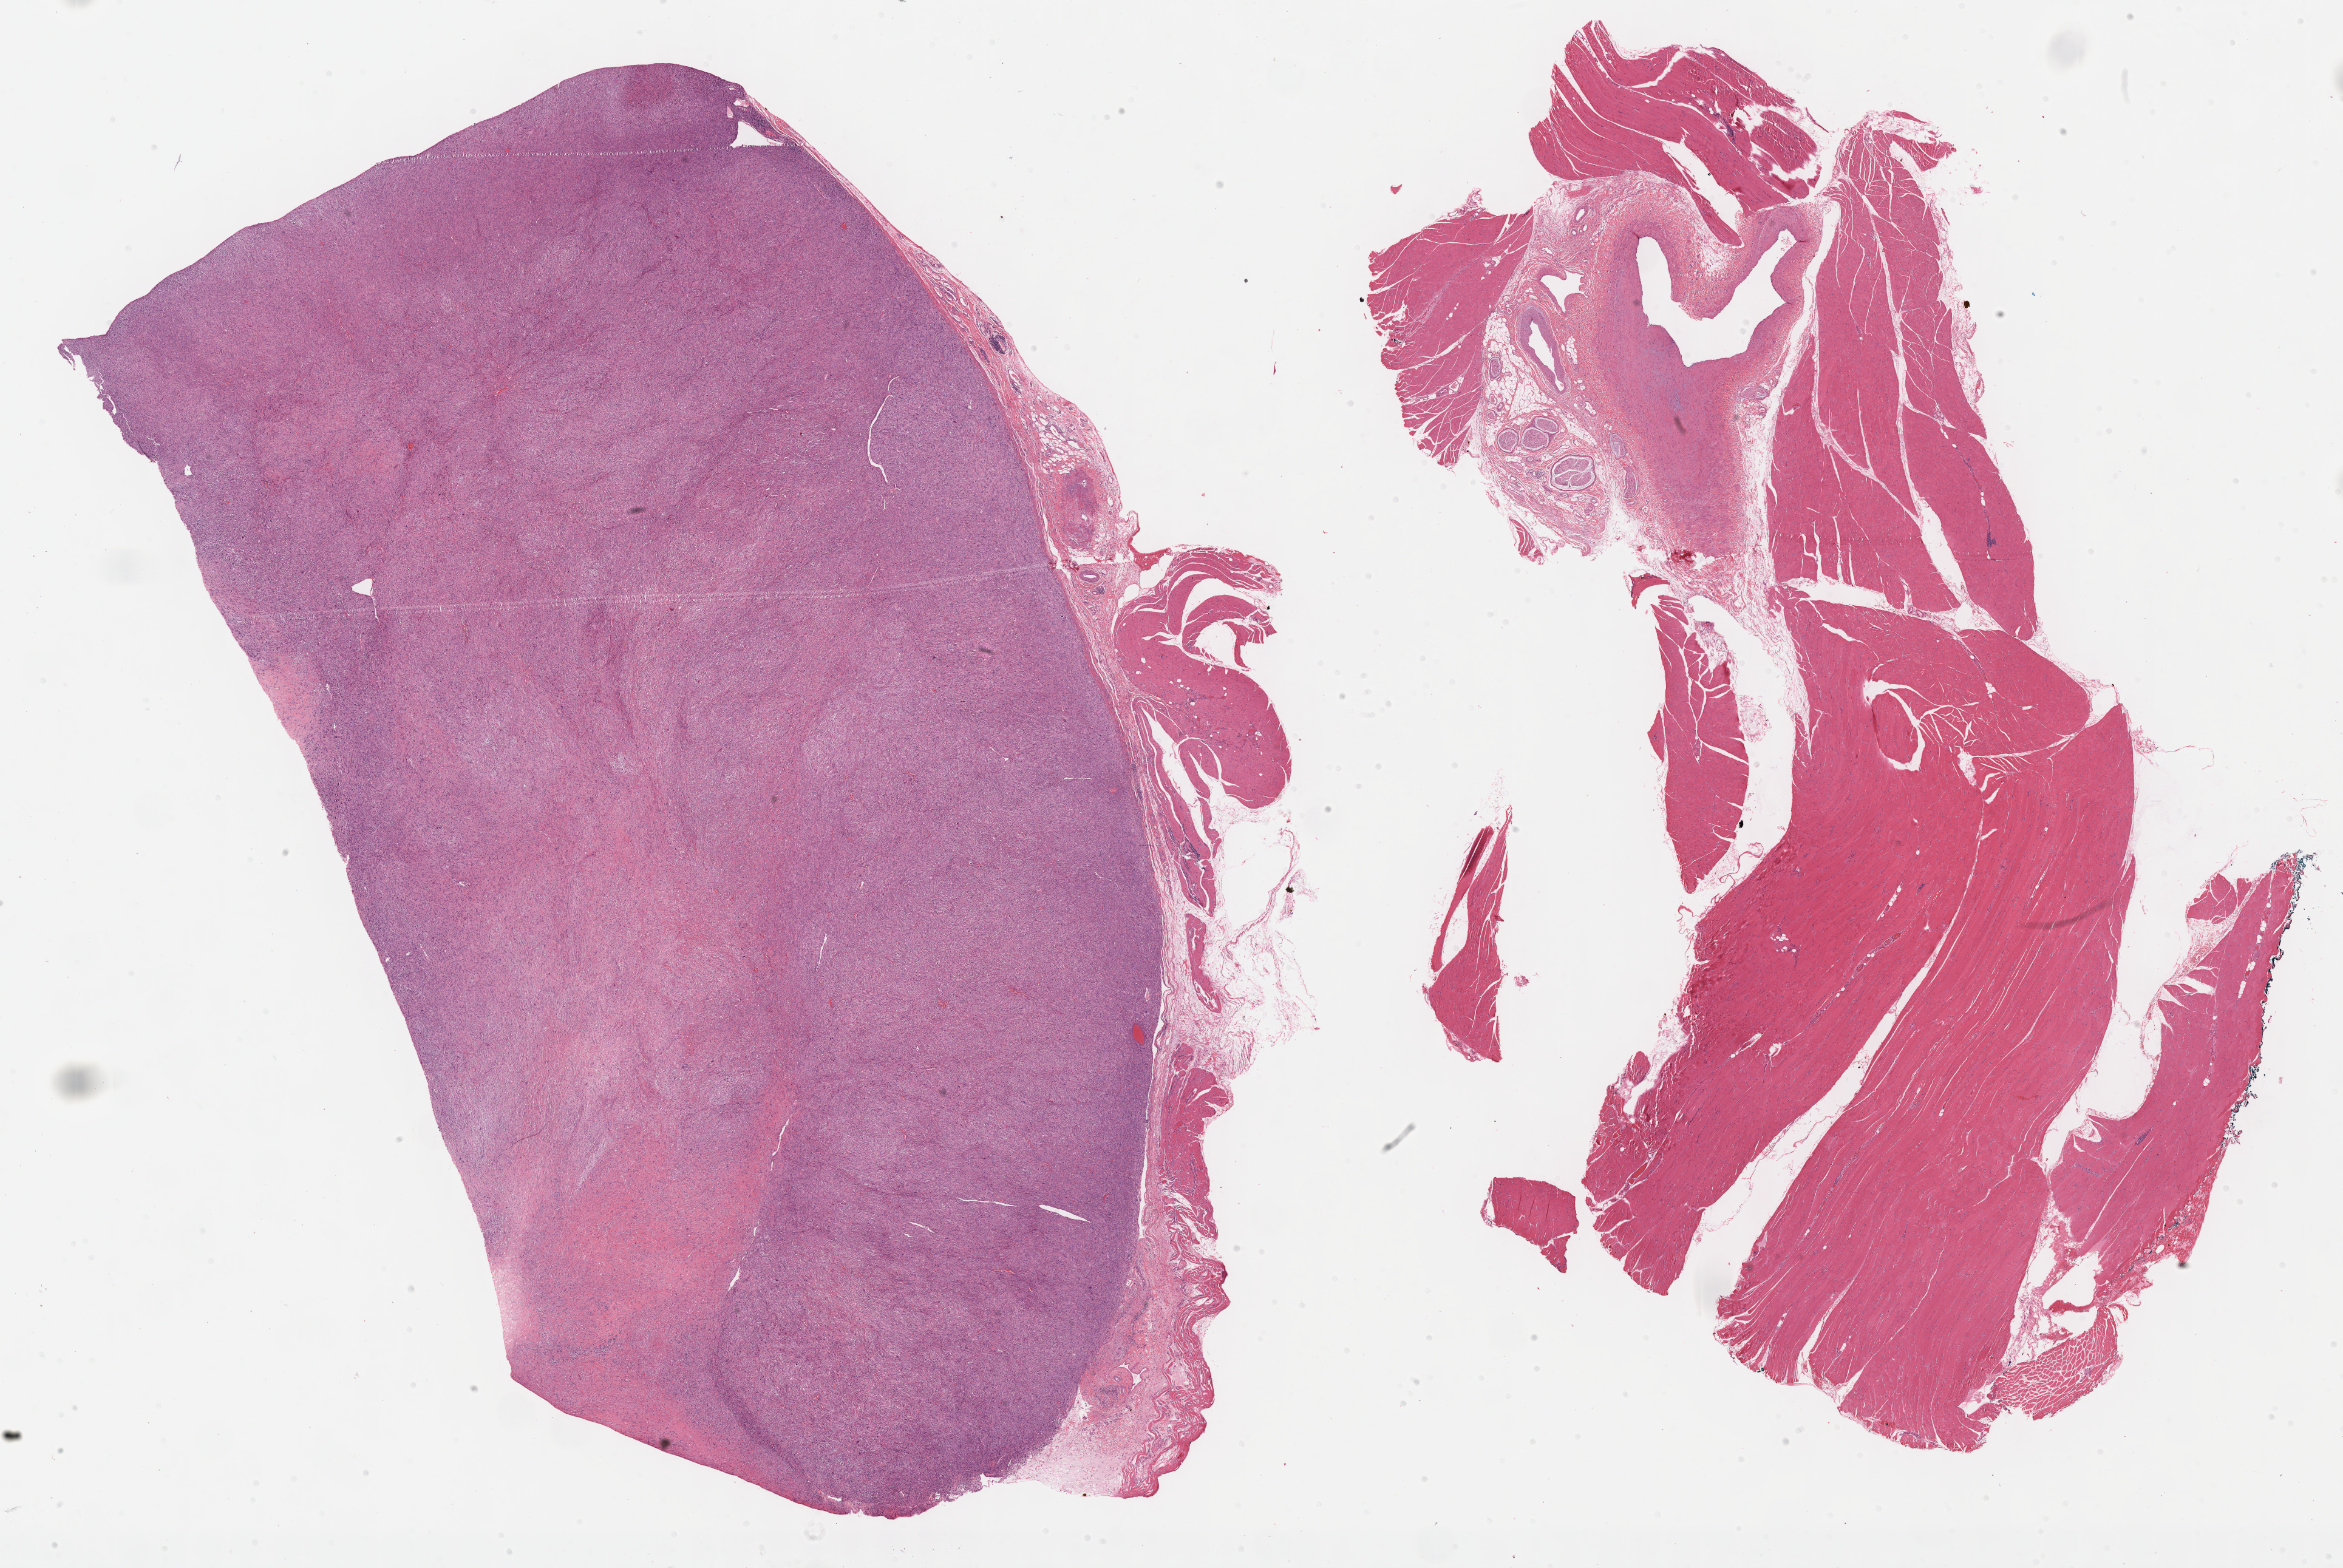
H&E whole-slide image — shown as a low-resolution overview of the whole scanned area (about 31.2 x 20.9 mm), formalin-fixed paraffin-embedded (FFPE) diagnostic section, connective, subcutaneous and other soft tissues, primary tumour sample. Patient: female, age at initial diagnosis 62 years.
Pathologic diagnosis: Malignant fibrous histiocytoma.